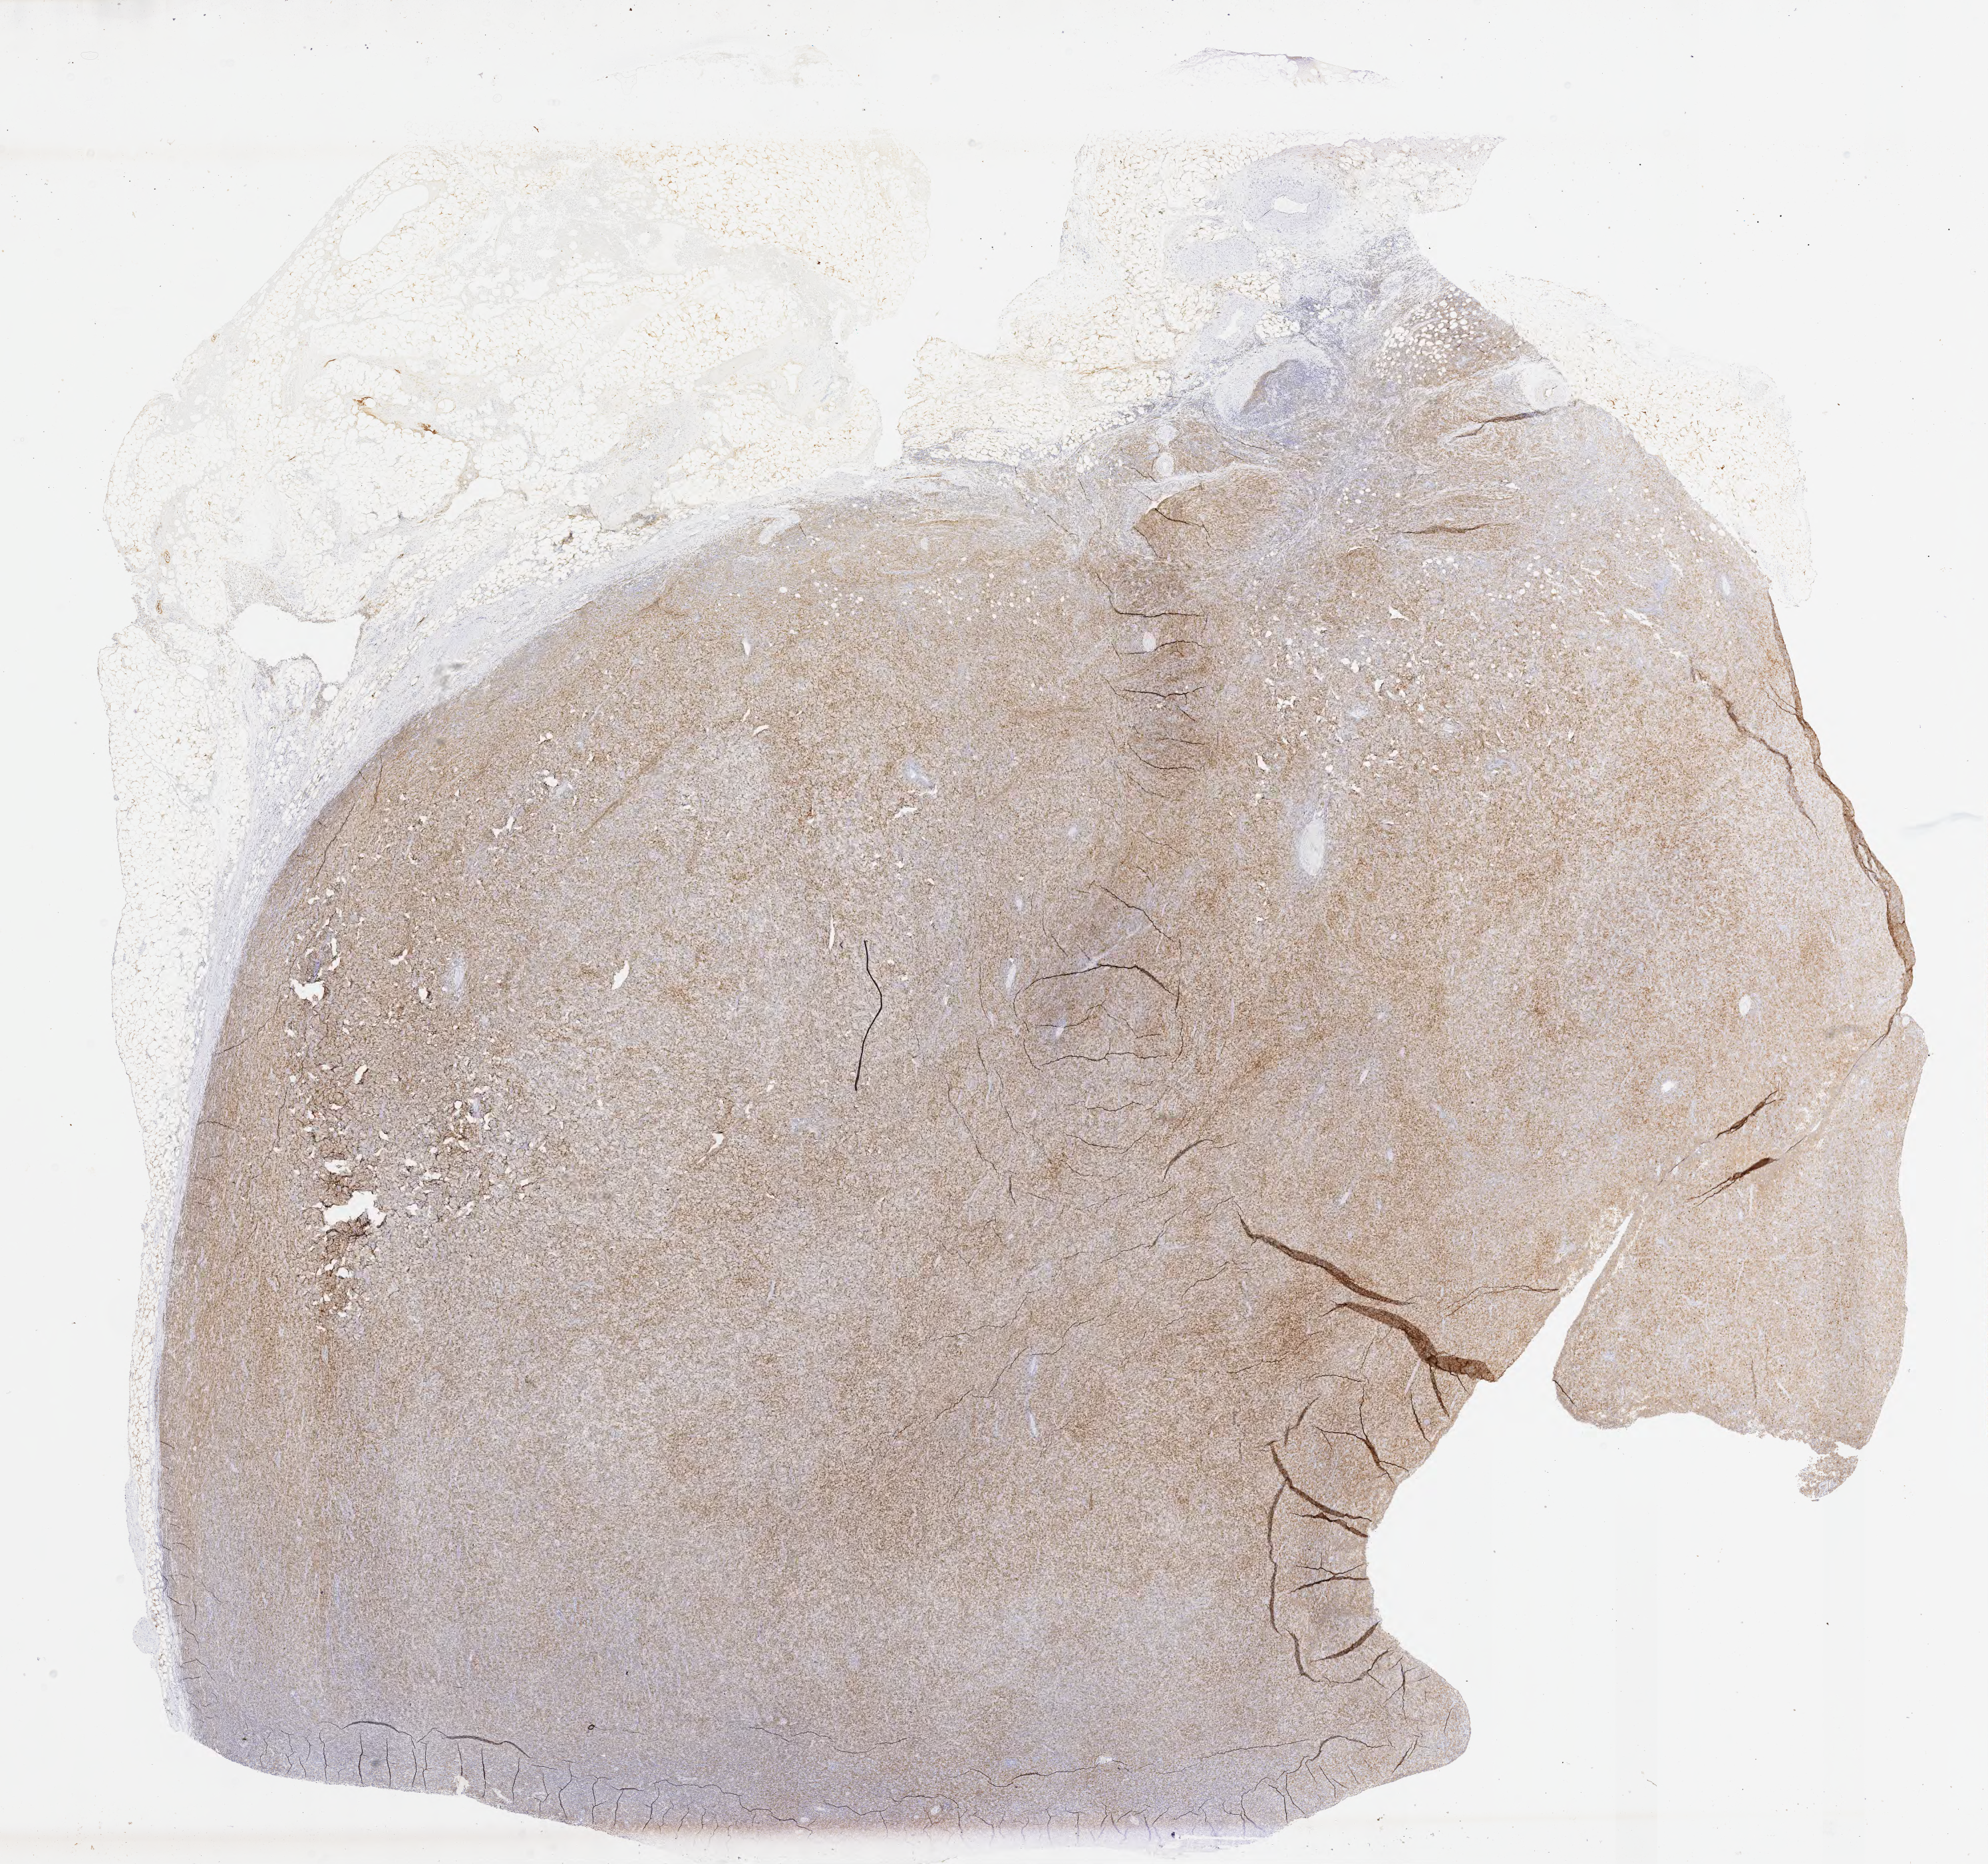
Whole-slide image, immunohistochemical stain for CD10, a low-resolution overview of the entire scanned area, about 24.1 x 22.6 mm. Tumor tissue. Site: lymph node. Male patient, aged 54.
Diagnosis: Diffuse large B-cell lymphoma, NOS.